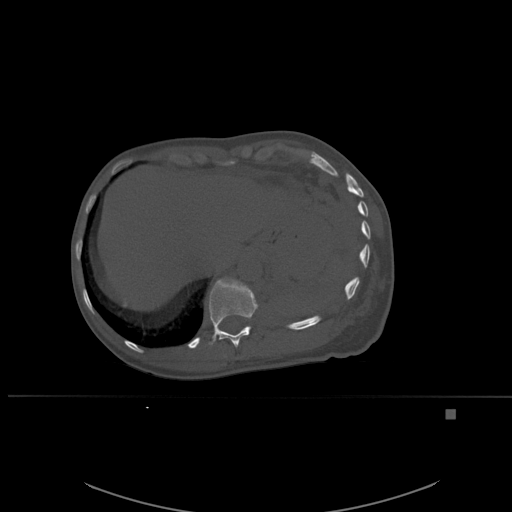
CT including the spine, one axial slice. Position 298 of 537 along the scan axis. Bone window (W 1800 / L 400 HU). 1.5 mm slice thickness. 512 × 512 image matrix, field of view 440 × 440 mm. Patient: female, 45 years. From the clinical record (not read from this slice): primary cancer: lung.
Annotated regions visible in this slice (semi-automatically segmented with operator editing):
- T11 vertebra: bounding box (x1, y1, x2, y2) in pixels: (209, 277, 258, 348)